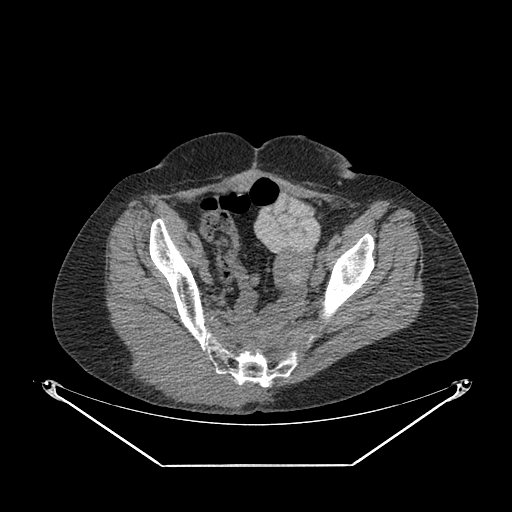
CT of an extremity soft-tissue mass (from a PET/CT study), one axial slice; position 66 of 267 along the scan axis; reconstruction kernel SOFT; 140 kVp; soft-tissue window (W 400 / L 40 HU); 3.75 mm slice thickness; 512 × 512 image matrix, field of view 500 × 500 mm. Female patient. From the clinical record (not read from this slice): histological type: spindle cell suggestive of myxofibrosarcoma; grade: intermediate; site of the primary tumour: right buttock.
Outlined on this slice (expert contour drawn on MRI and transferred to this co-registered scan by the dataset authors):
- gross tumour volume (mass): box from (x=123, y=326) to (x=250, y=410) px